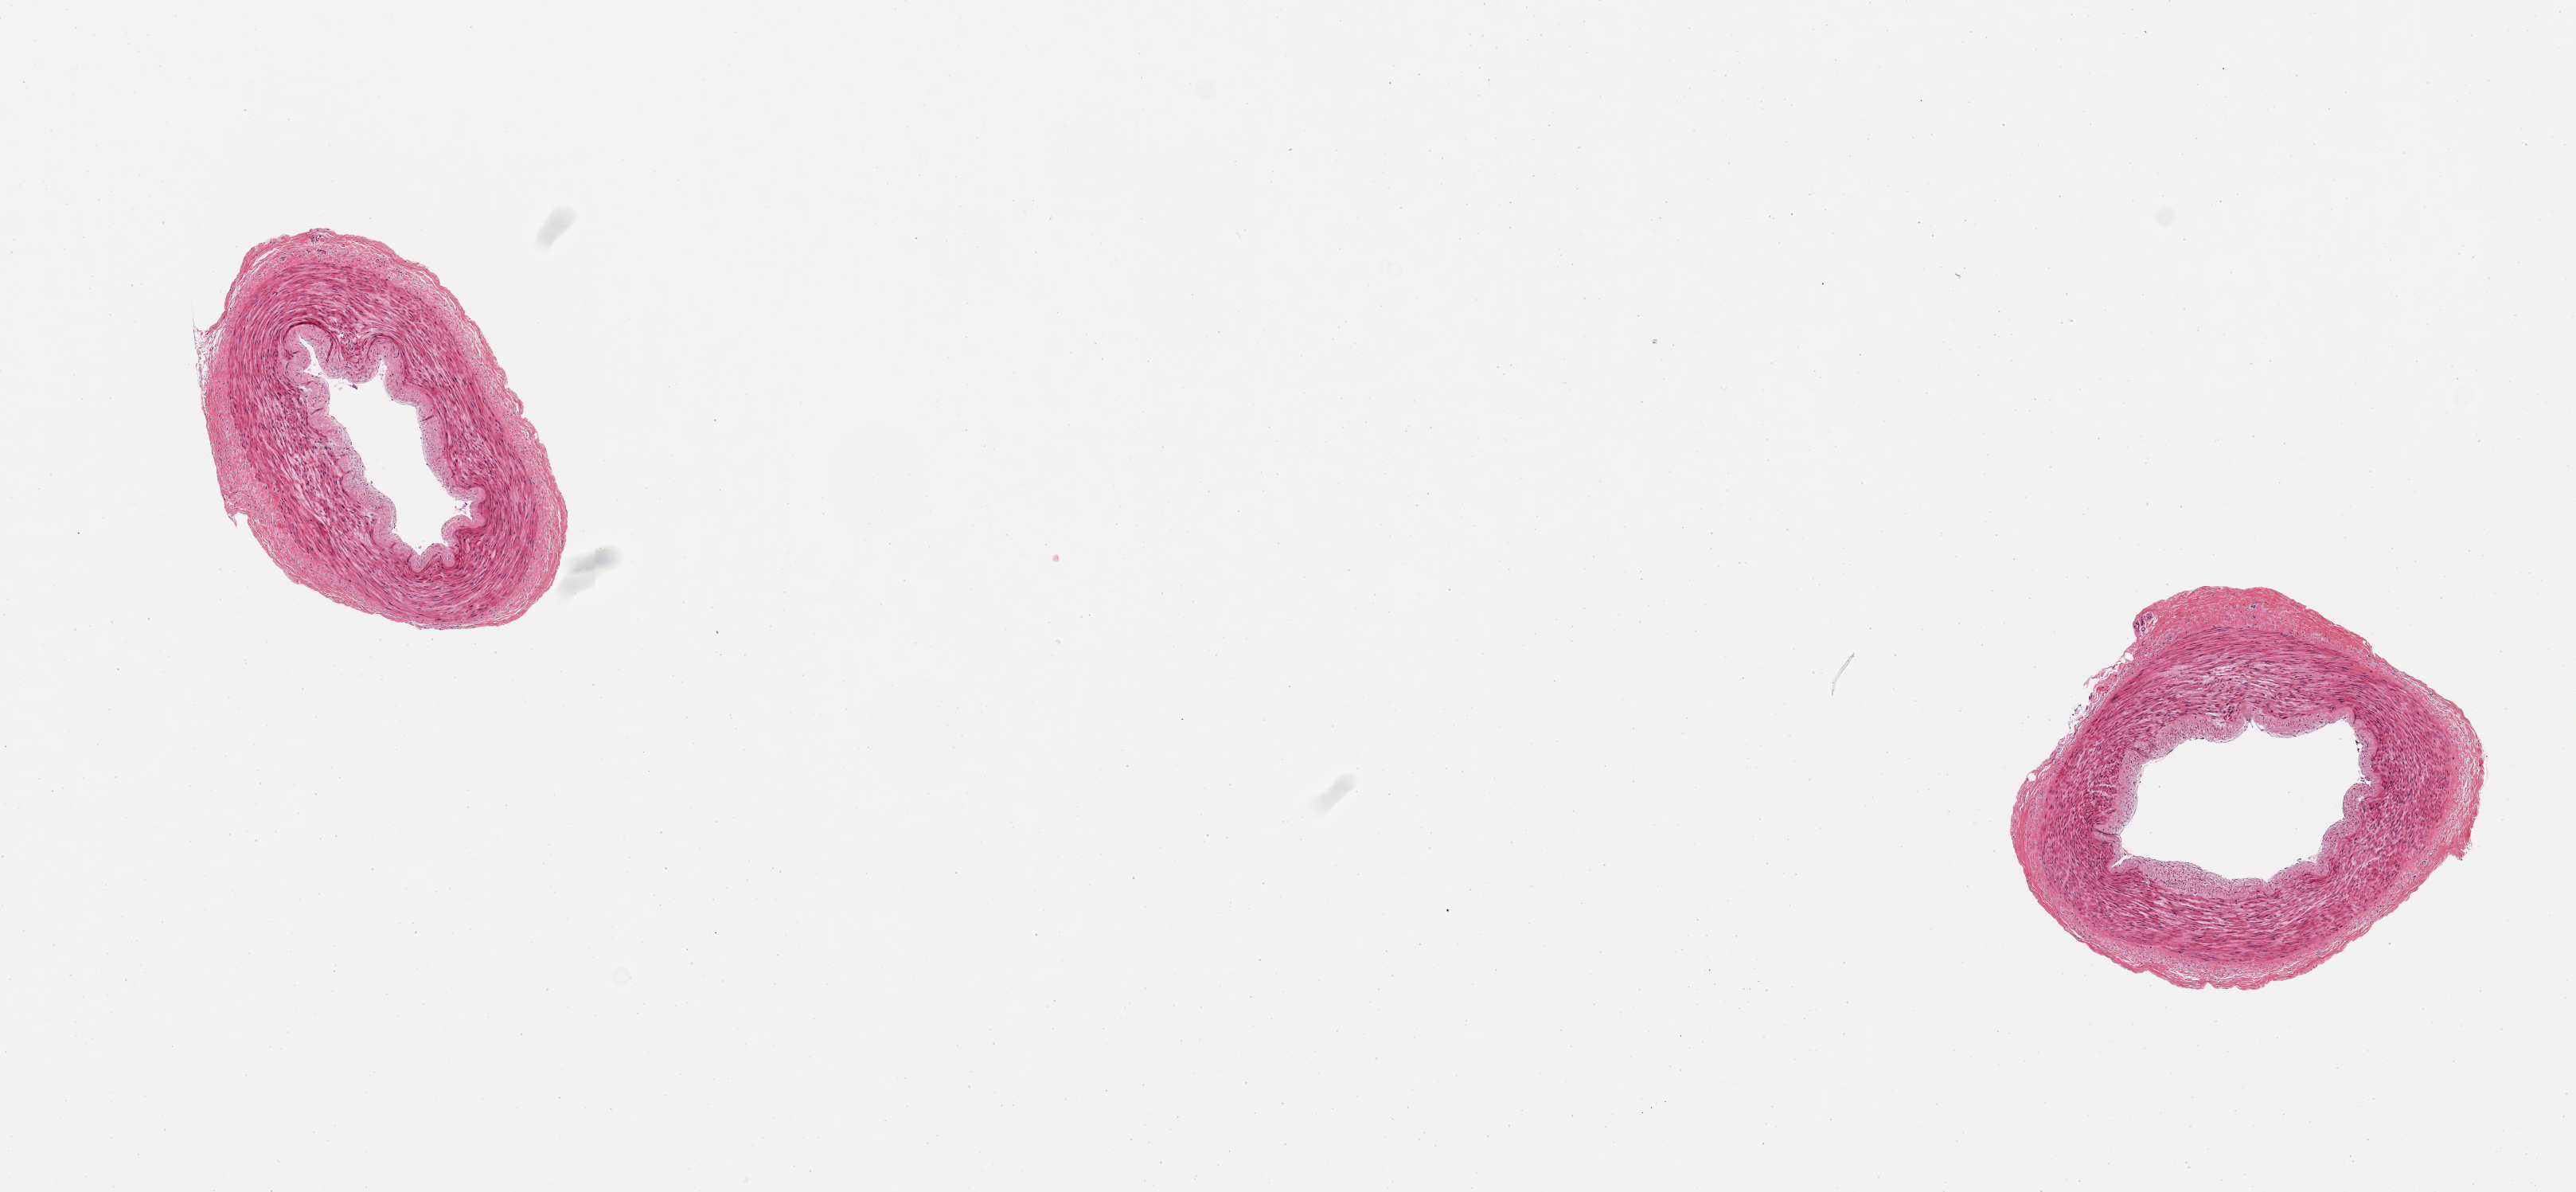
Whole-slide image, hematoxylin and eosin (H&E) stain, whole scanned area (about 12.8 x 5.9 mm) shown as a low-resolution overview, PAXgene-fixed paraffin-embedded (PFPE) section, sampled site (target tissue): tibial artery, tissue donor sample. Female donor.
• reviewer comment on this tissue sample: 2 pieces; no plaques; well trimmed